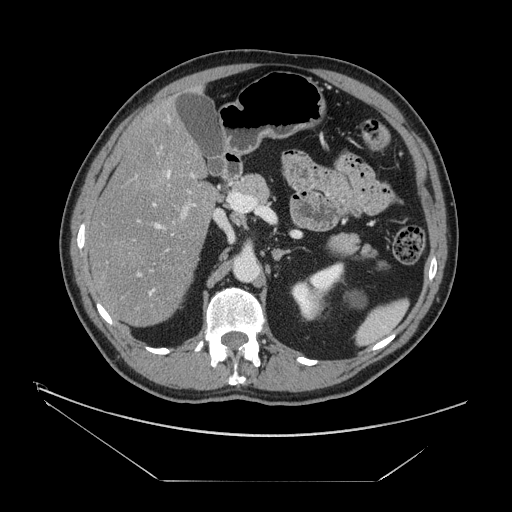
Contrast-enhanced abdominal CT, one axial slice; slice 80 of 161 in the series (ordered by position); reconstruction kernel STANDARD; 120 kVp; intravenous contrast given; soft-tissue window (W 400 / L 40 HU); 2.5 mm slice thickness; 512 × 512 image matrix, field of view 440 × 440 mm. Male patient, age 65 years. Case-level facts recorded for this patient, not image findings: diagnosis: colorectal cancer liver metastases, imaged before liver resection; multiple liver metastases: yes; largest metastasis: 4.2 cm; disease in both lobes: yes.
Annotated regions visible in this slice (expert manual segmentation):
- hepatic veins: bounding box <133,169,174,297> (left, top, right, bottom; pixels)
- liver: <89,100,217,327>
- planned liver remnant (the part of the liver to remain after resection): <105,101,208,326>
- portal vein (with intrahepatic branches): <112,152,203,324>